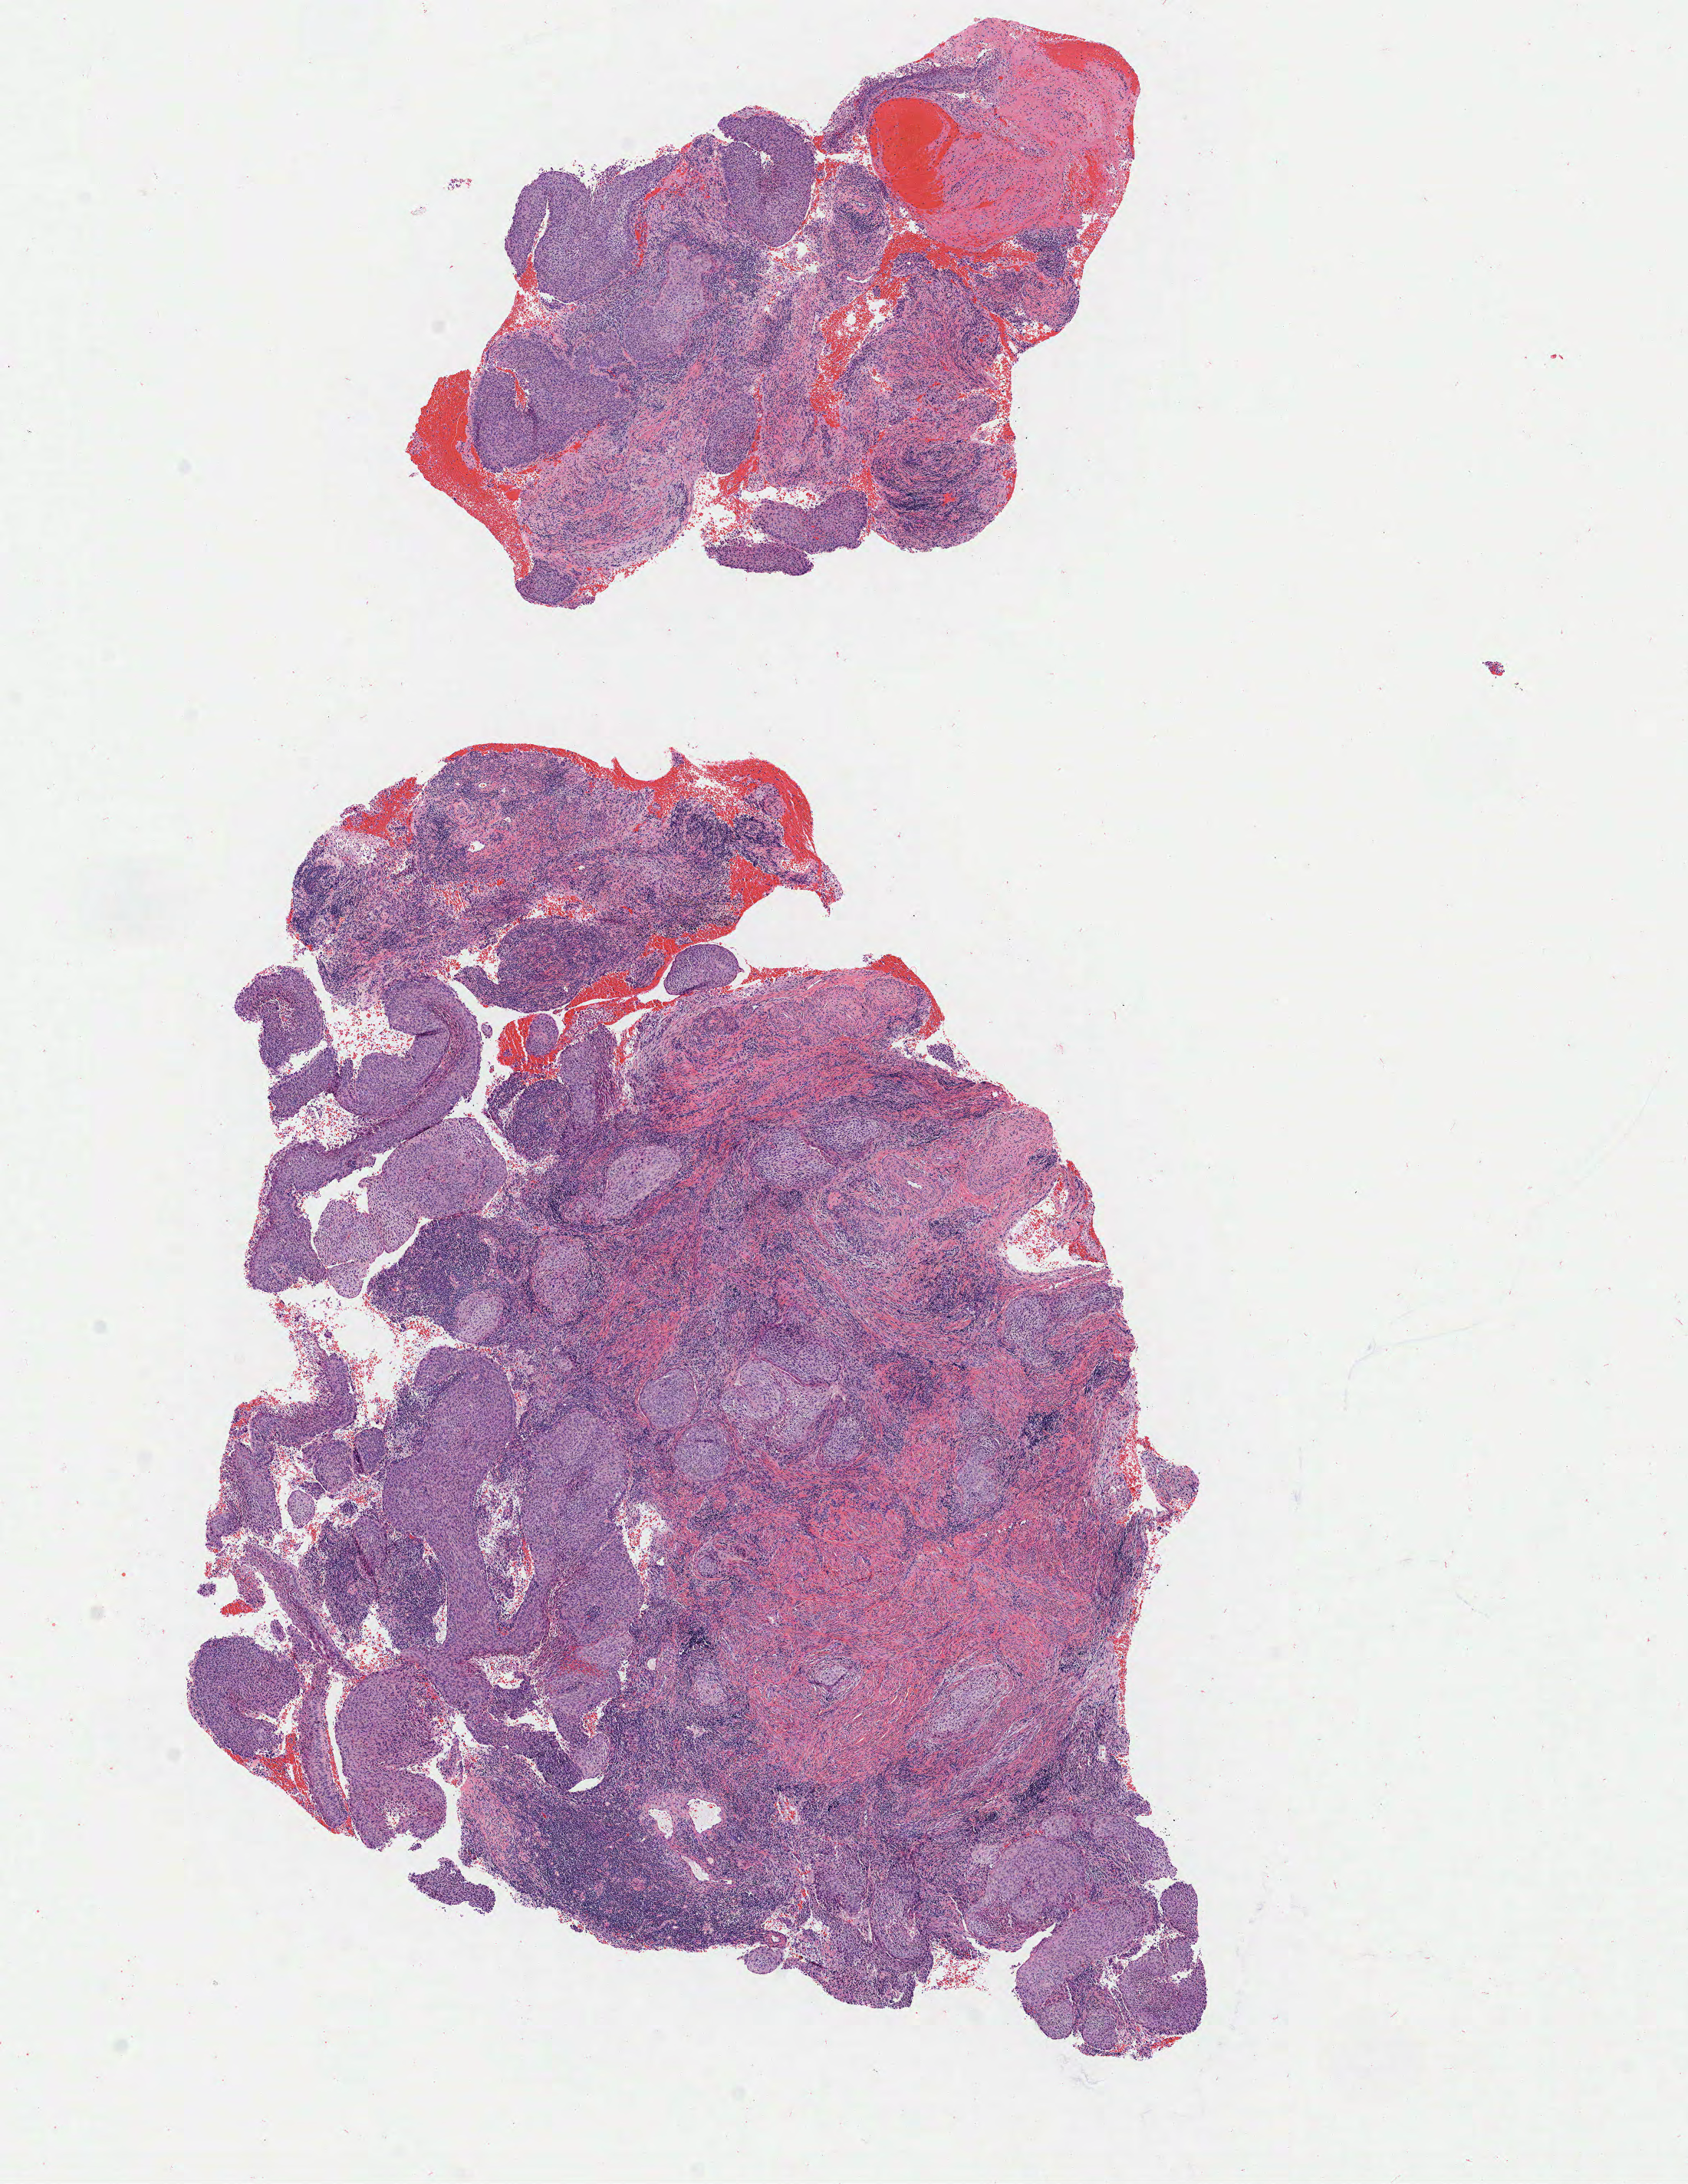
Hematoxylin and eosin (H&E) whole-slide image — whole scanned area (about 8.8 x 11.3 mm) shown as a low-resolution overview; tumor tissue; site: cervix. Female patient, 54 years old.
• histologic diagnosis: Squamous cell carcinoma, large cell, nonkeratinizing, NOS